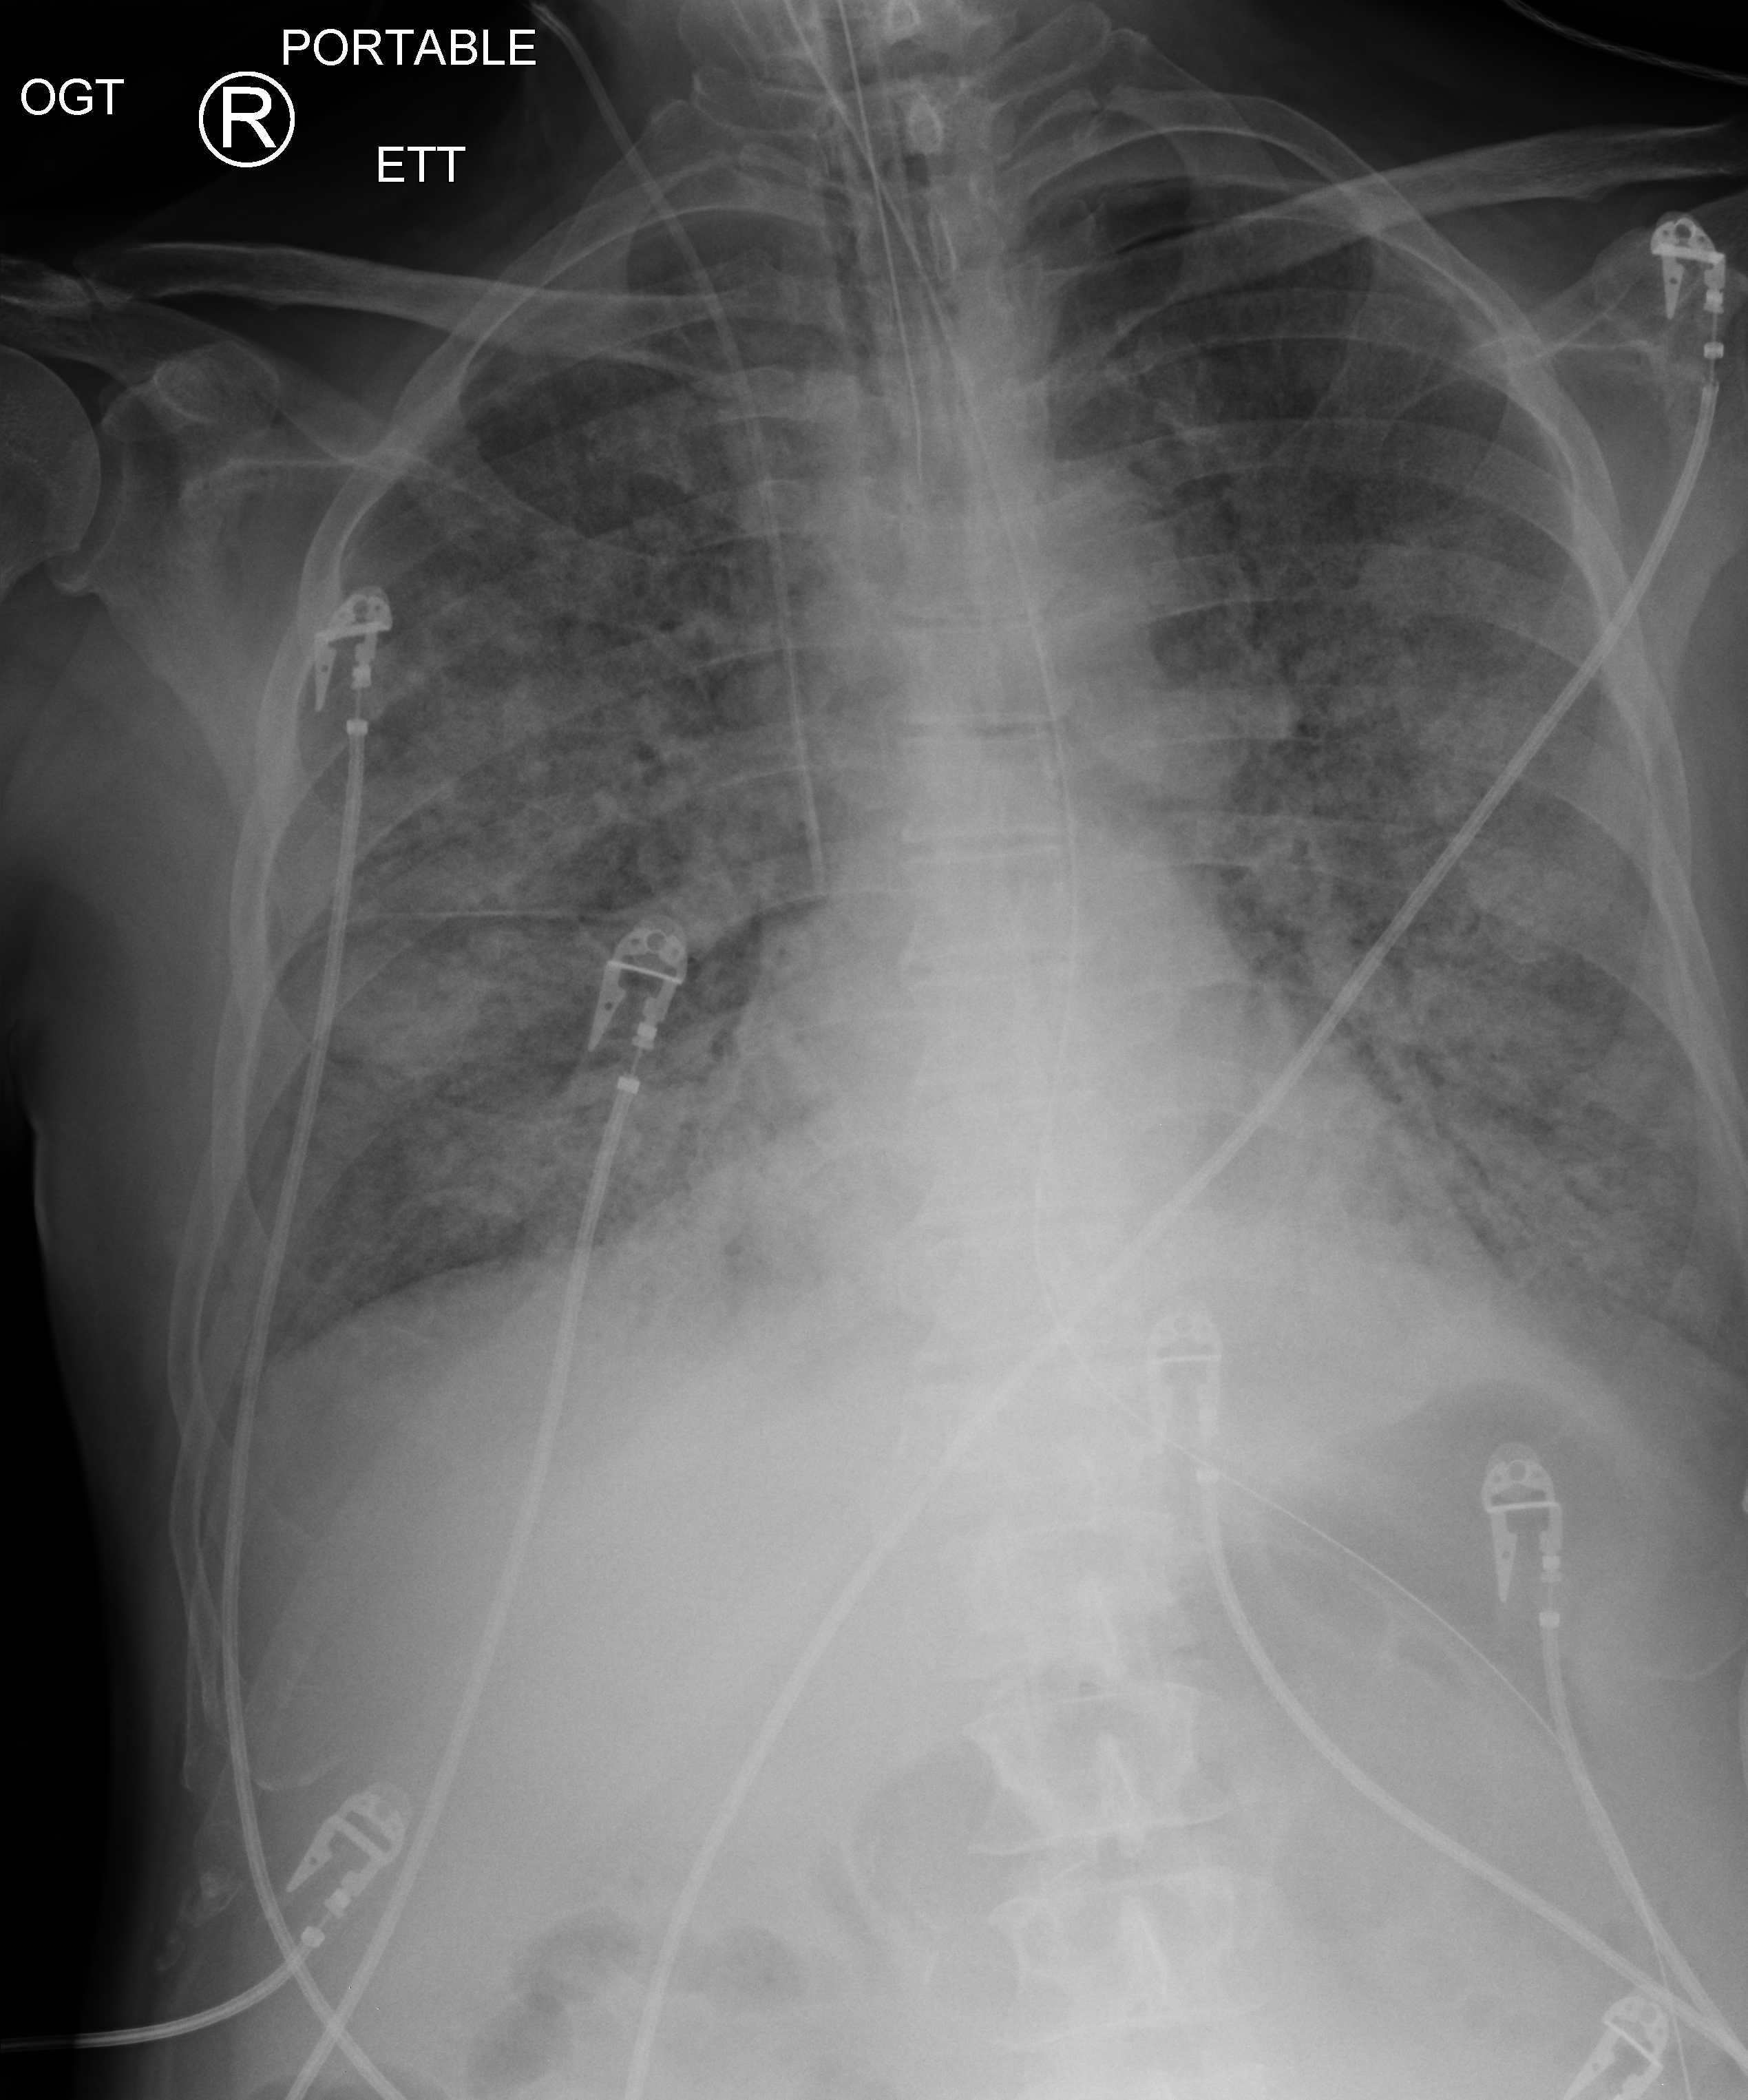
Chest X-ray (portable), anteroposterior (AP) projection. Patient hospitalised with COVID-19; male, aged 60–74 years.
Admission-level facts for this patient (not findings on this image; timing relative to this image not recorded):
- hypertension (admission record): no